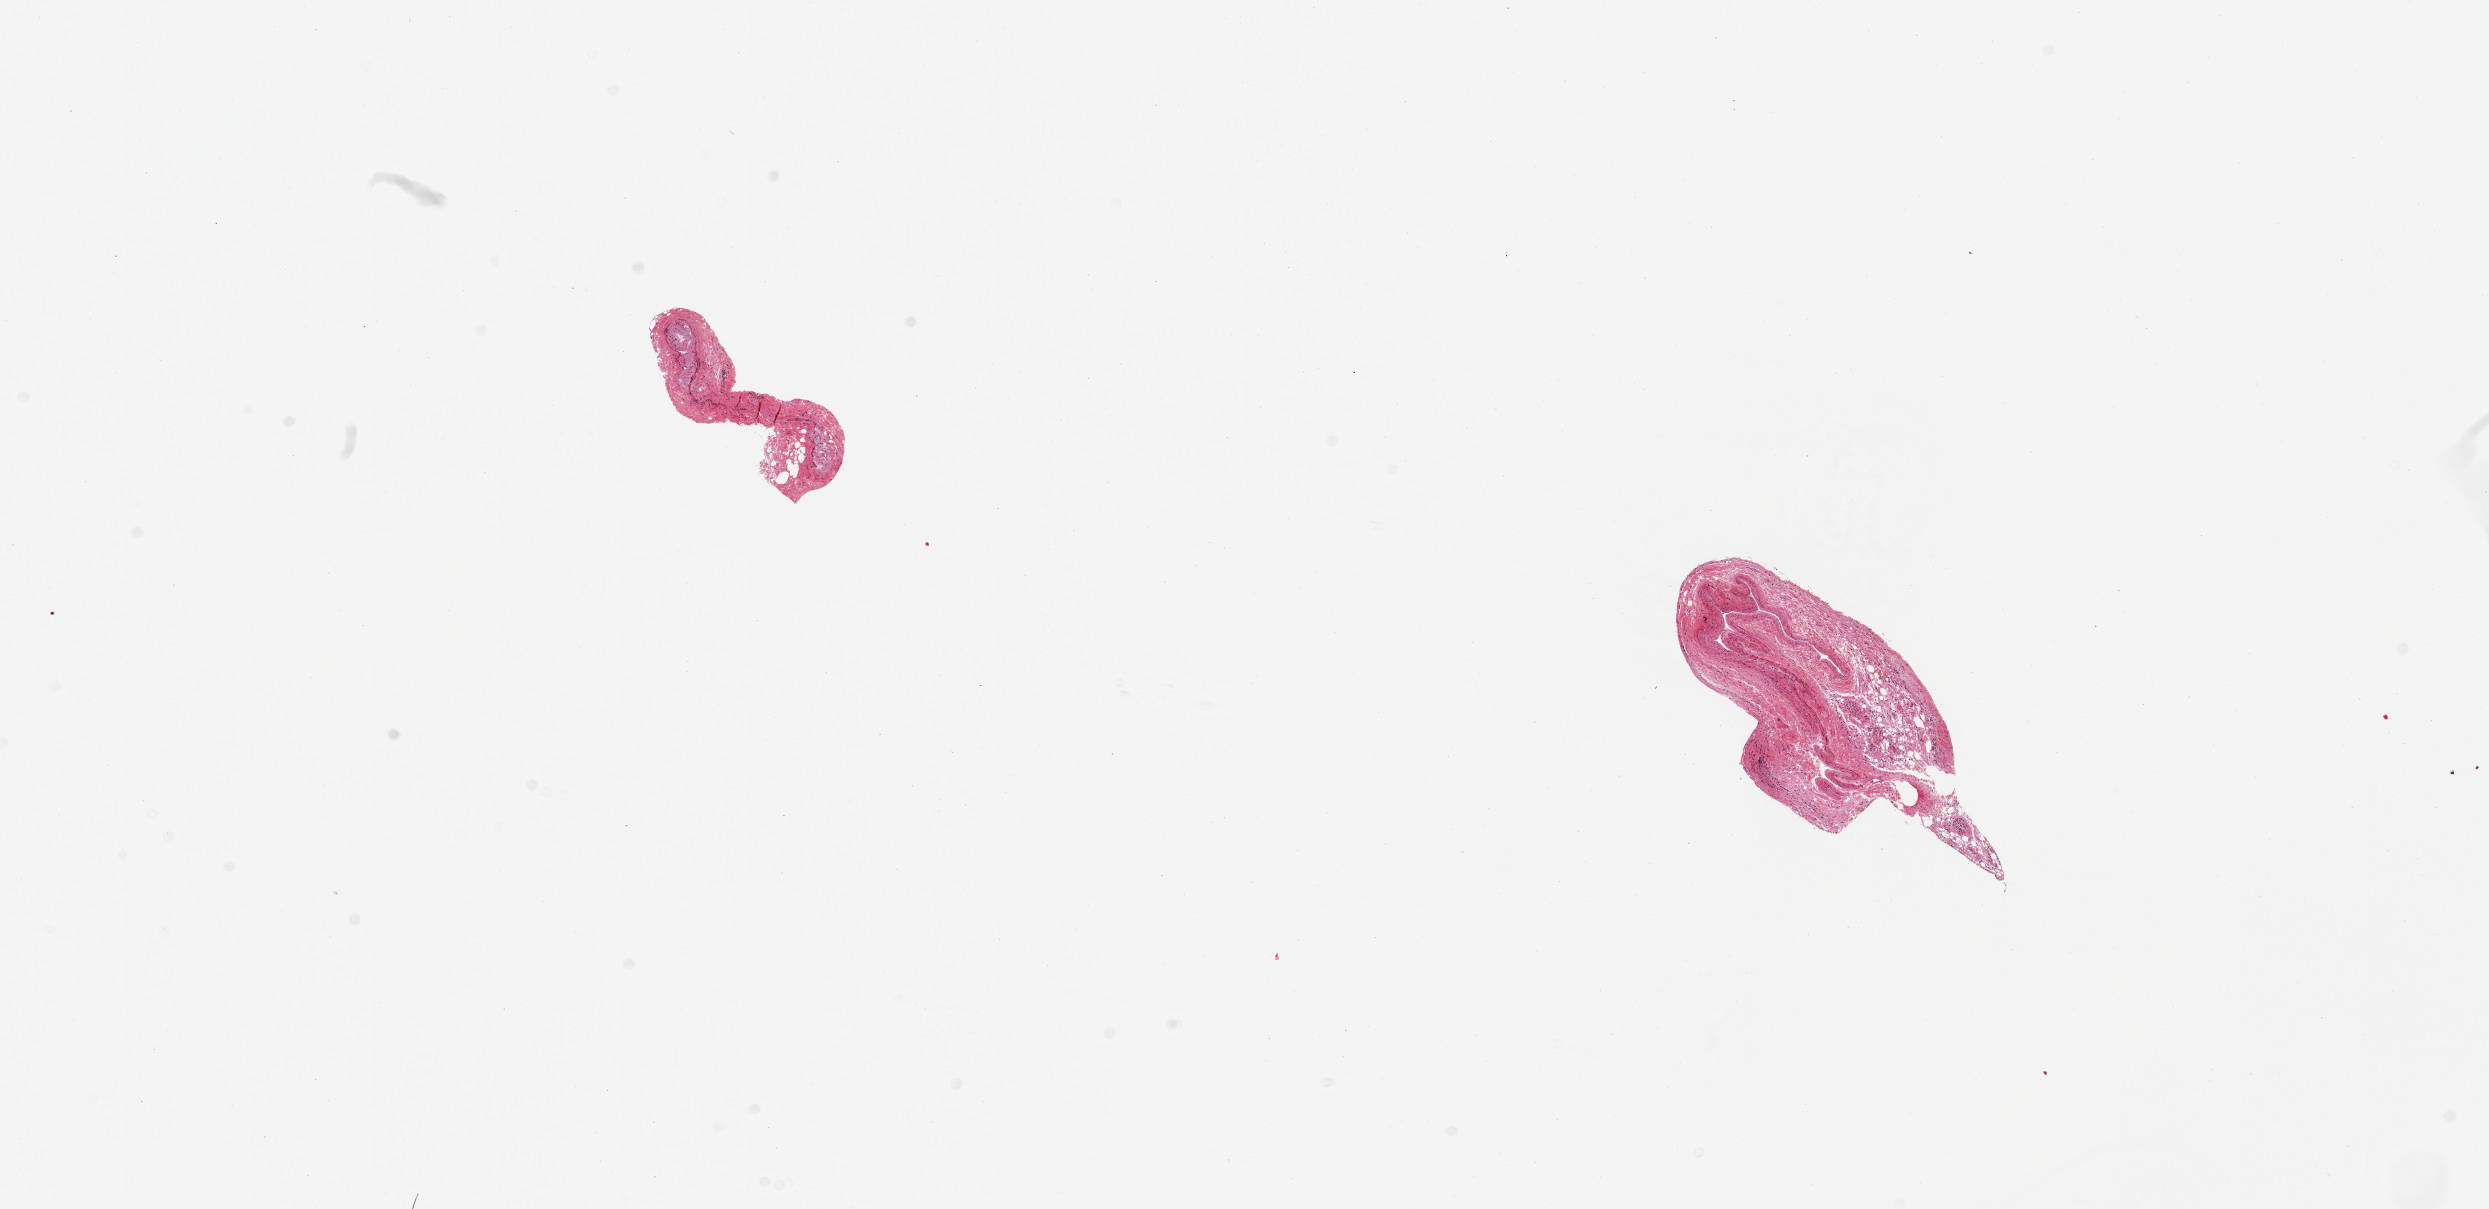
Digitized hematoxylin and eosin (H&E)-stained section, brightfield — a low-resolution overview of the entire scanned area, about 19.7 x 9.6 mm, PAXgene-fixed, paraffin-embedded tissue, section of coronary artery (target tissue), donor tissue sample. Donor sex: male.
* reviewer comment on this tissue sample: 2 pieces; samples appear to be veins